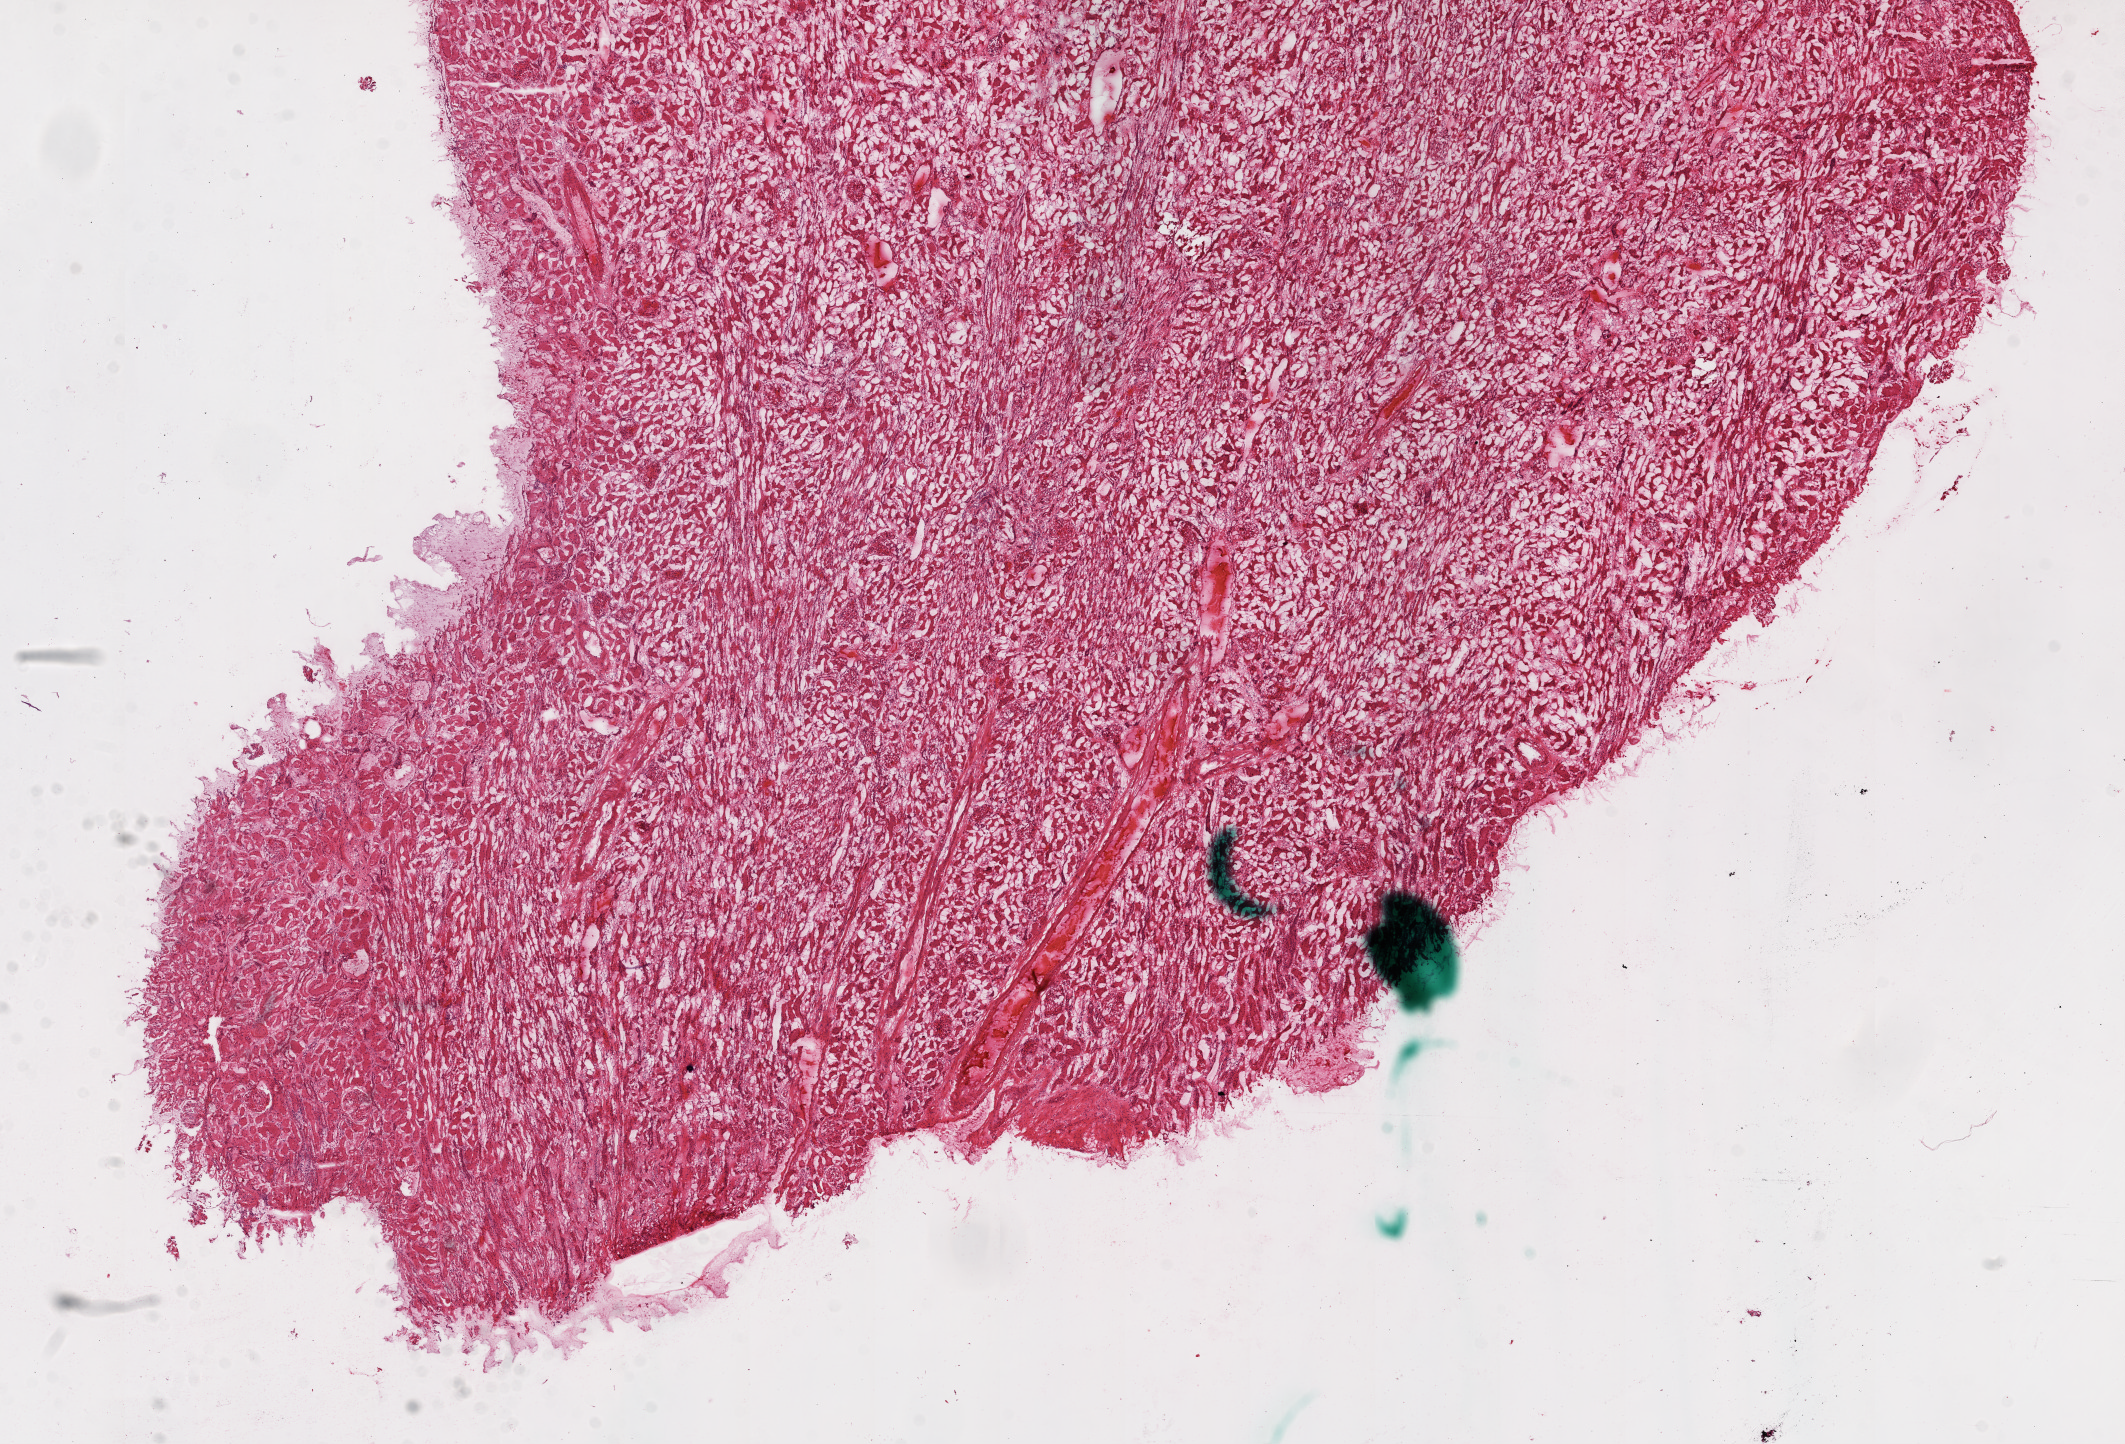
Whole-slide histology image, H&E-stained — shown as a low-resolution overview of the whole scanned area (about 17.1 x 11.6 mm, acquisition: 20x scan), frozen section from the top of the tissue portion, solid tissue normal (non-tumour tissue) sample from the kidney. Patient: male, age at initial diagnosis 43 years.
This section: solid tissue normal (non-tumour) sample from the same patient. Patient diagnosis: Clear cell adenocarcinoma, NOS.